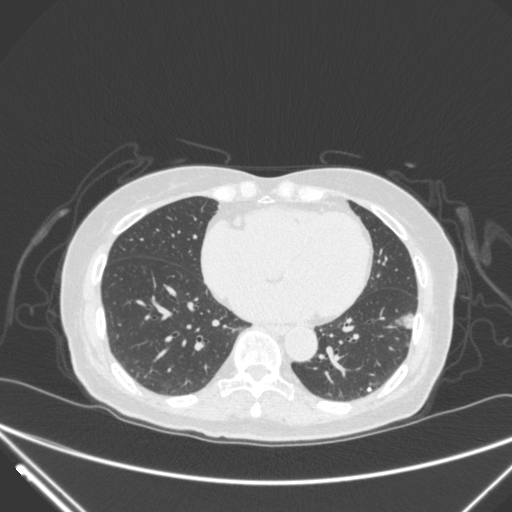
Chest CT, one axial slice; position 115 of 310 along the scan axis; 120 kVp; lung window (W 1500 / L -600 HU); 1 mm slice thickness; 512 × 512 image matrix, field of view 377 × 377 mm. Female patient, age 82 years. From the clinical record (not read from this slice): clinical TNM (as recorded): T1c N0 M0; histopathological grade: G2.
Structures marked on this image (bounding box drawn by a radiologist):
- lung tumour (recorded histology: adenocarcinoma): bounding box [x1, y1, x2, y2] px = [387, 303, 424, 345]